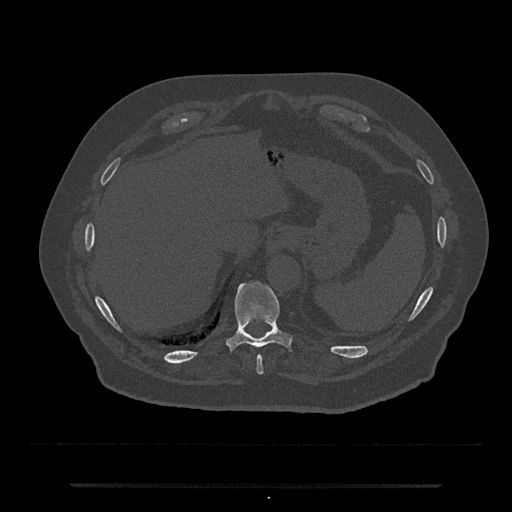
CT including the spine, one axial slice. Slice 709 of 797 in the series (ordered by position). Reconstruction kernel Br40s/3. 120 kVp. Bone window (W 1800 / L 400 HU). 0.5 mm slice thickness. 512 × 512 image matrix, field of view 434 × 434 mm. Male patient, age 80 years. Case-level facts recorded for this patient, not image findings: primary cancer: prostate.
Annotated regions visible in this slice (semi-automatic segmentation, software-assisted and operator-edited):
- T10 vertebra: bounding box (x1, y1, x2, y2) in pixels: (226, 282, 292, 350)
- T9 vertebra: (256, 356, 264, 375)